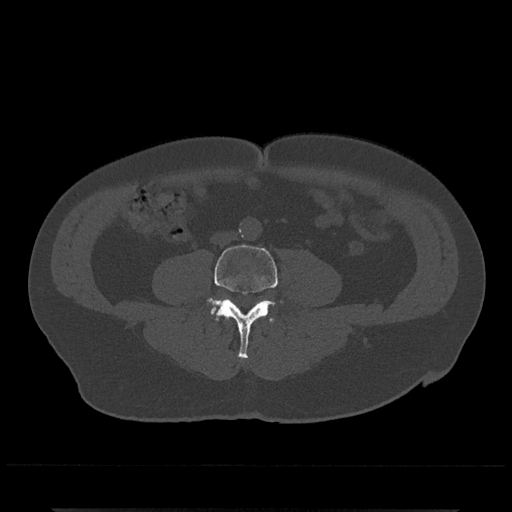
CT including the spine, one axial slice; slice 146 of 797 in the series (ordered by position); bone window (W 1800 / L 400 HU); 0.5 mm slice thickness; 512 × 512 image matrix, field of view 393 × 393 mm. Patient: male, 67 years. From the clinical record (not read from this slice): primary cancer: prostate.
Annotated regions visible in this slice (semi-automatic segmentation, software-assisted and operator-edited):
- L4 vertebra: bounding box <207,244,282,359> (left, top, right, bottom; pixels)
- L5 vertebra: <211,305,216,314>